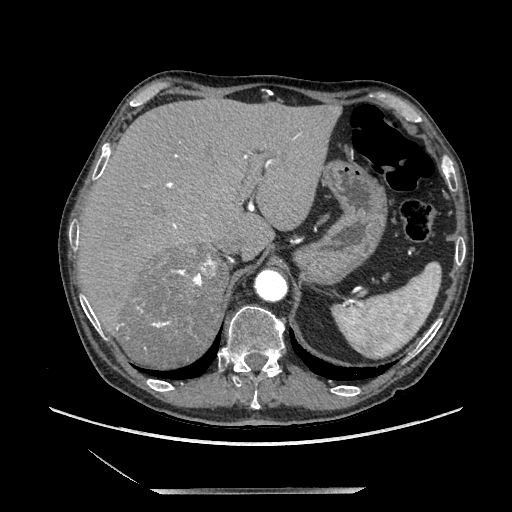
Contrast-enhanced abdominal CT, one axial slice. Position 161 of 243 along the scan axis. Soft-tissue window (W 400 / L 40 HU). 1.25 mm slice thickness. 512 × 512 image matrix. Male patient. Case-level facts recorded for this patient, not image findings: diagnosis: adrenocortical carcinoma; tumour side: right adrenal; tumour size at pathology: 16 cm.
Outlined on this slice (semi-automatic segmentation, software-assisted and operator-edited):
- mass: bounding box [x1, y1, x2, y2] px = [122, 246, 225, 370]